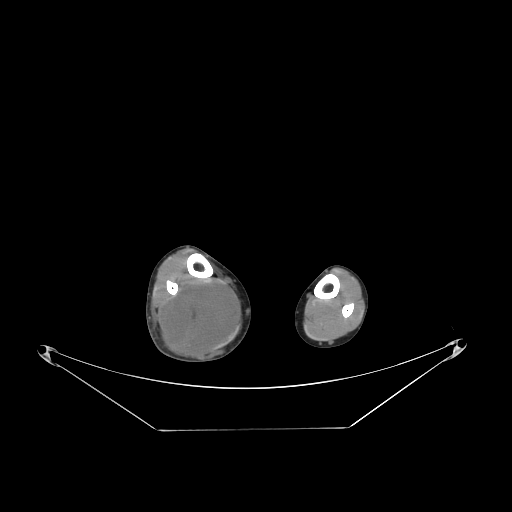
CT of an extremity soft-tissue mass (from a PET/CT study), one axial slice; slice 75 of 267 in the series (ordered by position); soft-tissue window (W 400 / L 40 HU); 3.75 mm slice thickness; 512 × 512 image matrix, field of view 500 × 500 mm. Male patient. From the clinical record (not read from this slice): histological type: liposarcoma - round cell; grade: high; site of the primary tumour: right calf.
Annotated regions visible in this slice (expert contour drawn on MRI and transferred to this co-registered scan by the dataset authors):
- gross tumour volume (mass): bounding box (x1, y1, x2, y2) in pixels: (160, 279, 239, 364)